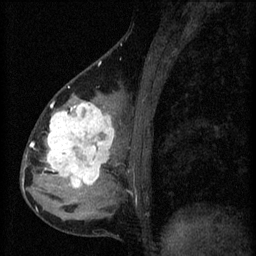
Breast MRI (dynamic contrast-enhanced), one sagittal slice. Position 22 of 60 along the scan axis. 3 images stored at this slice position (order not interpretable as contrast timing). 1.5 T. TE 4.2 ms, TR 8.2 ms. 256 × 256 image matrix, field of view 180 × 180 mm. Female patient, age 37 years.
Structures marked on this image (semi-automatic segmentation, software-assisted and operator-edited):
- analysis volume of interest (the breast-tissue region the enhancement analysis was run in; not a lesion): bounding box (x1, y1, x2, y2) in pixels: (44, 100, 119, 197)
- tumour enhancement mask (voxels above the 70 % enhancement threshold inside the analysis volume of interest): (45, 102, 115, 189)